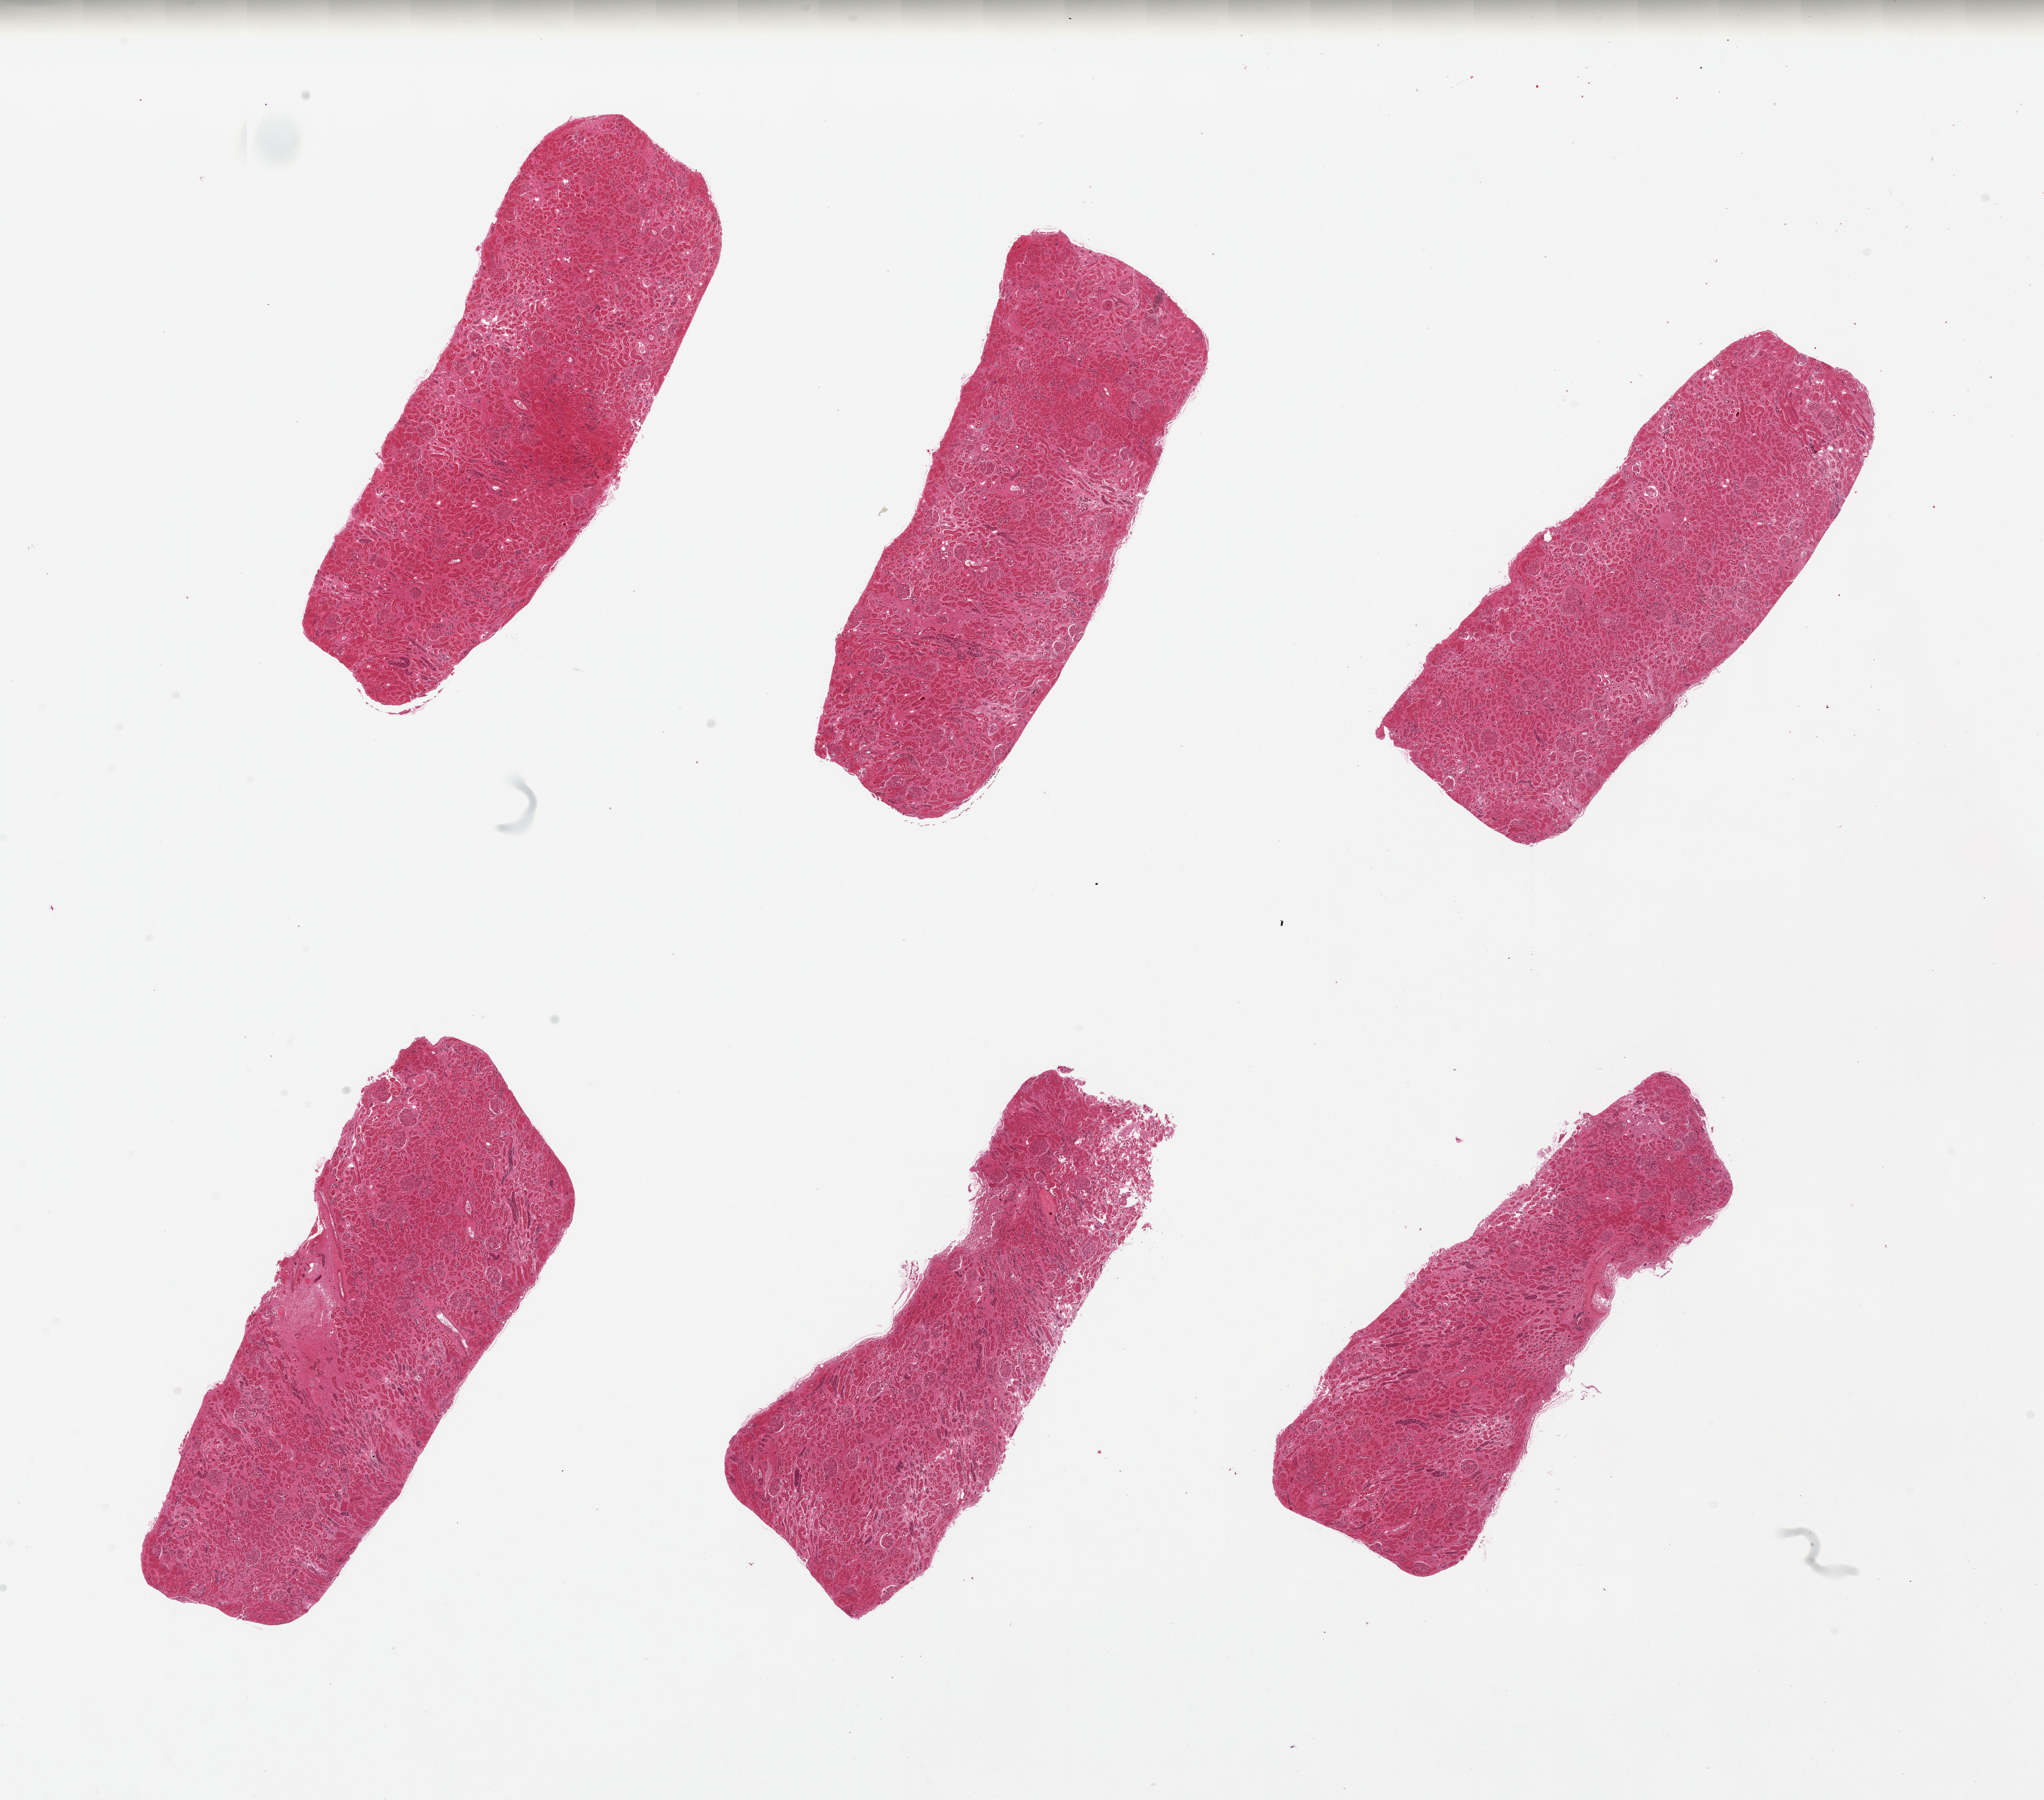
Digitized haematoxylin and eosin-stained section — low-resolution overview of the scanned area, about 24.6 x 21.7 mm (from a 20x scan), PAXgene-fixed paraffin-embedded (PFPE) section, section of renal cortex (target tissue), tissue donor sample. Male donor.
Reviewer comment on this tissue sample: 6 pieces. Tubules very autolyzed; cannot distinguish from acute tubular necrosis.